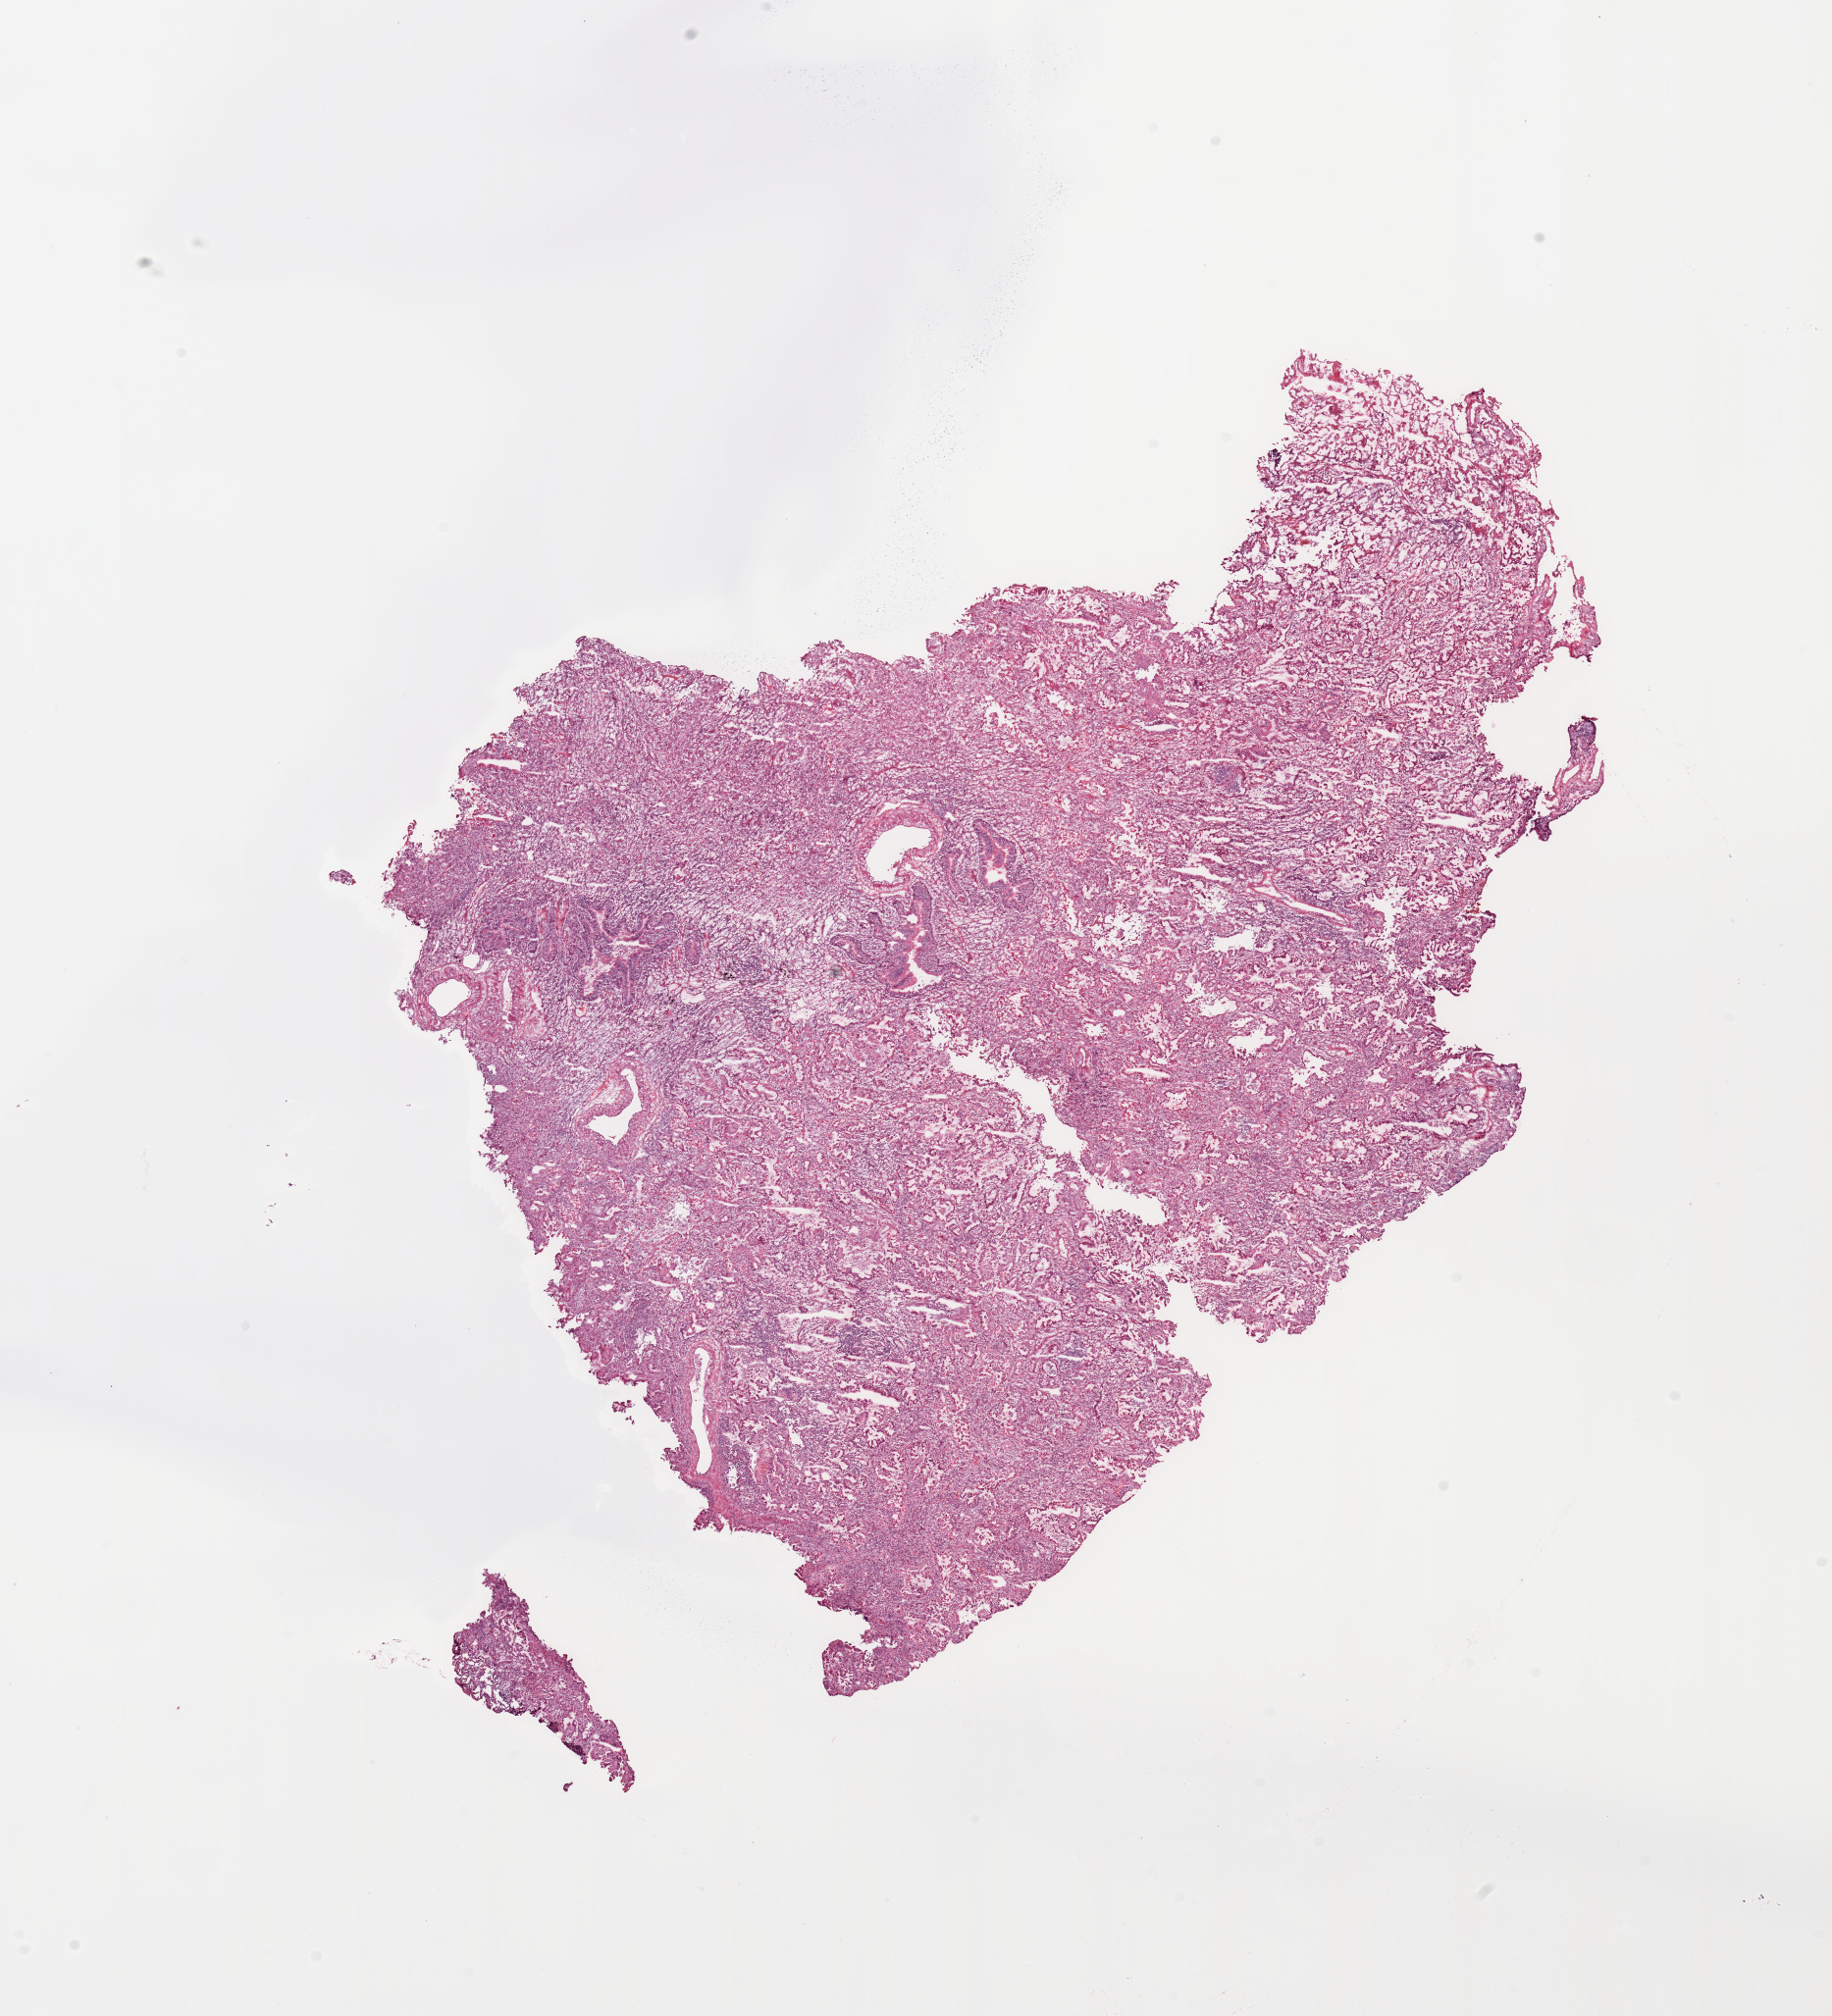
Whole-slide histology image, H&E — shown as a low-resolution overview of the whole scanned area (about 14.8 x 16.3 mm); lung, tumour tissue. Patient: male, age 79 years. Histologic grade: G2 (moderately differentiated).
Histologic diagnosis: Adenocarcinoma, NOS. Primary tumour site (as recorded): right lower lobe. AJCC pathologic stage: IIA.